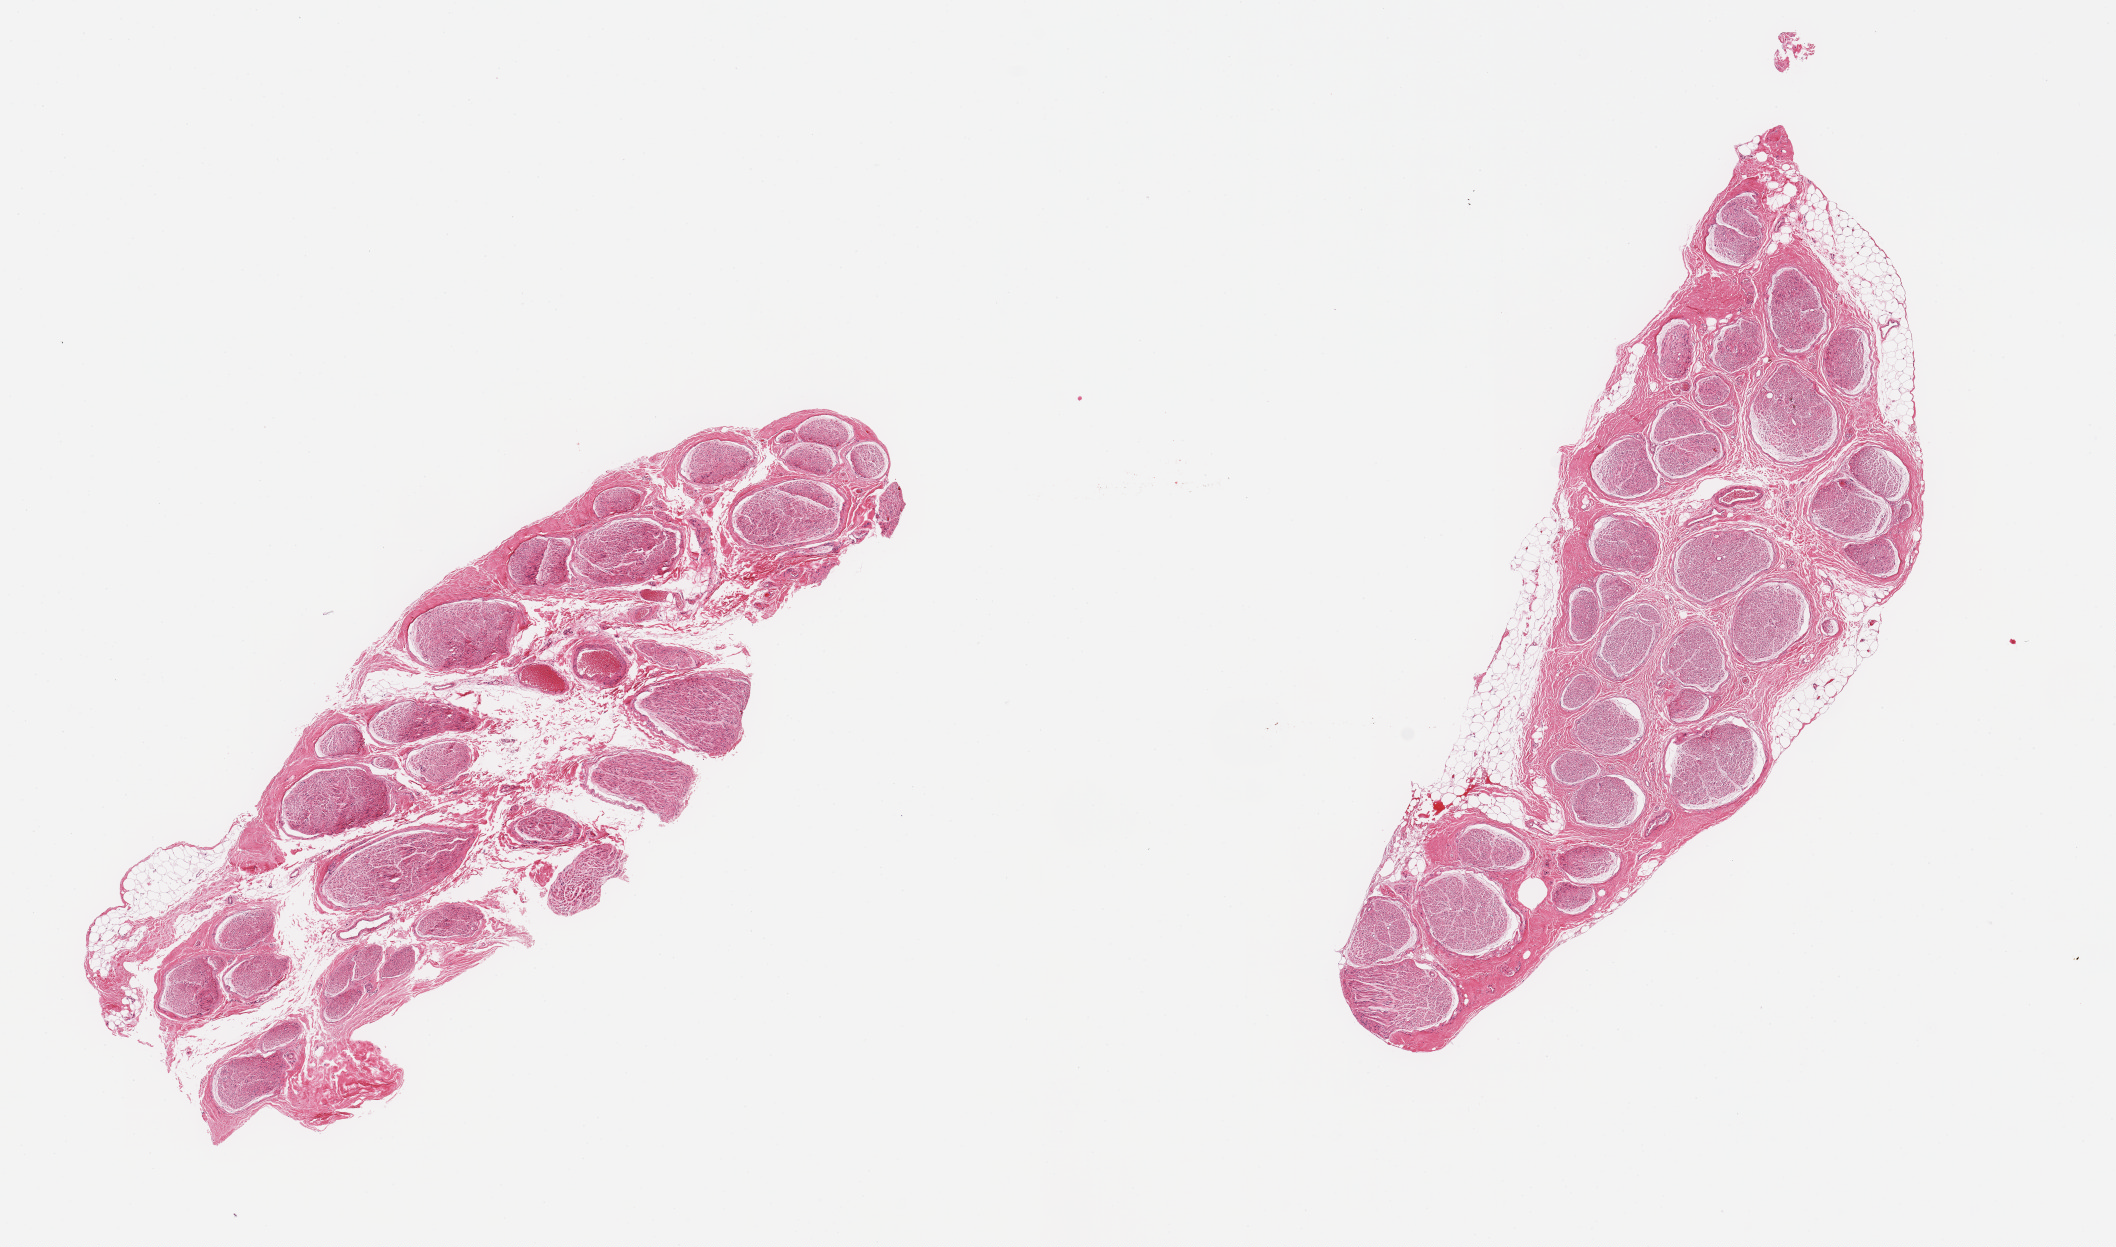
Whole-slide image, H&E stain, brightfield — a low-resolution overview of the entire scanned area, about 16.7 x 9.9 mm (acquisition: 20x scan); PAXgene-fixed paraffin-embedded (PFPE) section; section of tibial nerve (target tissue); donor tissue sample. Donor: male.
Pathologist's review note for this sample: 2 pieces, trace nubbins of fat up to ~0.3mm.